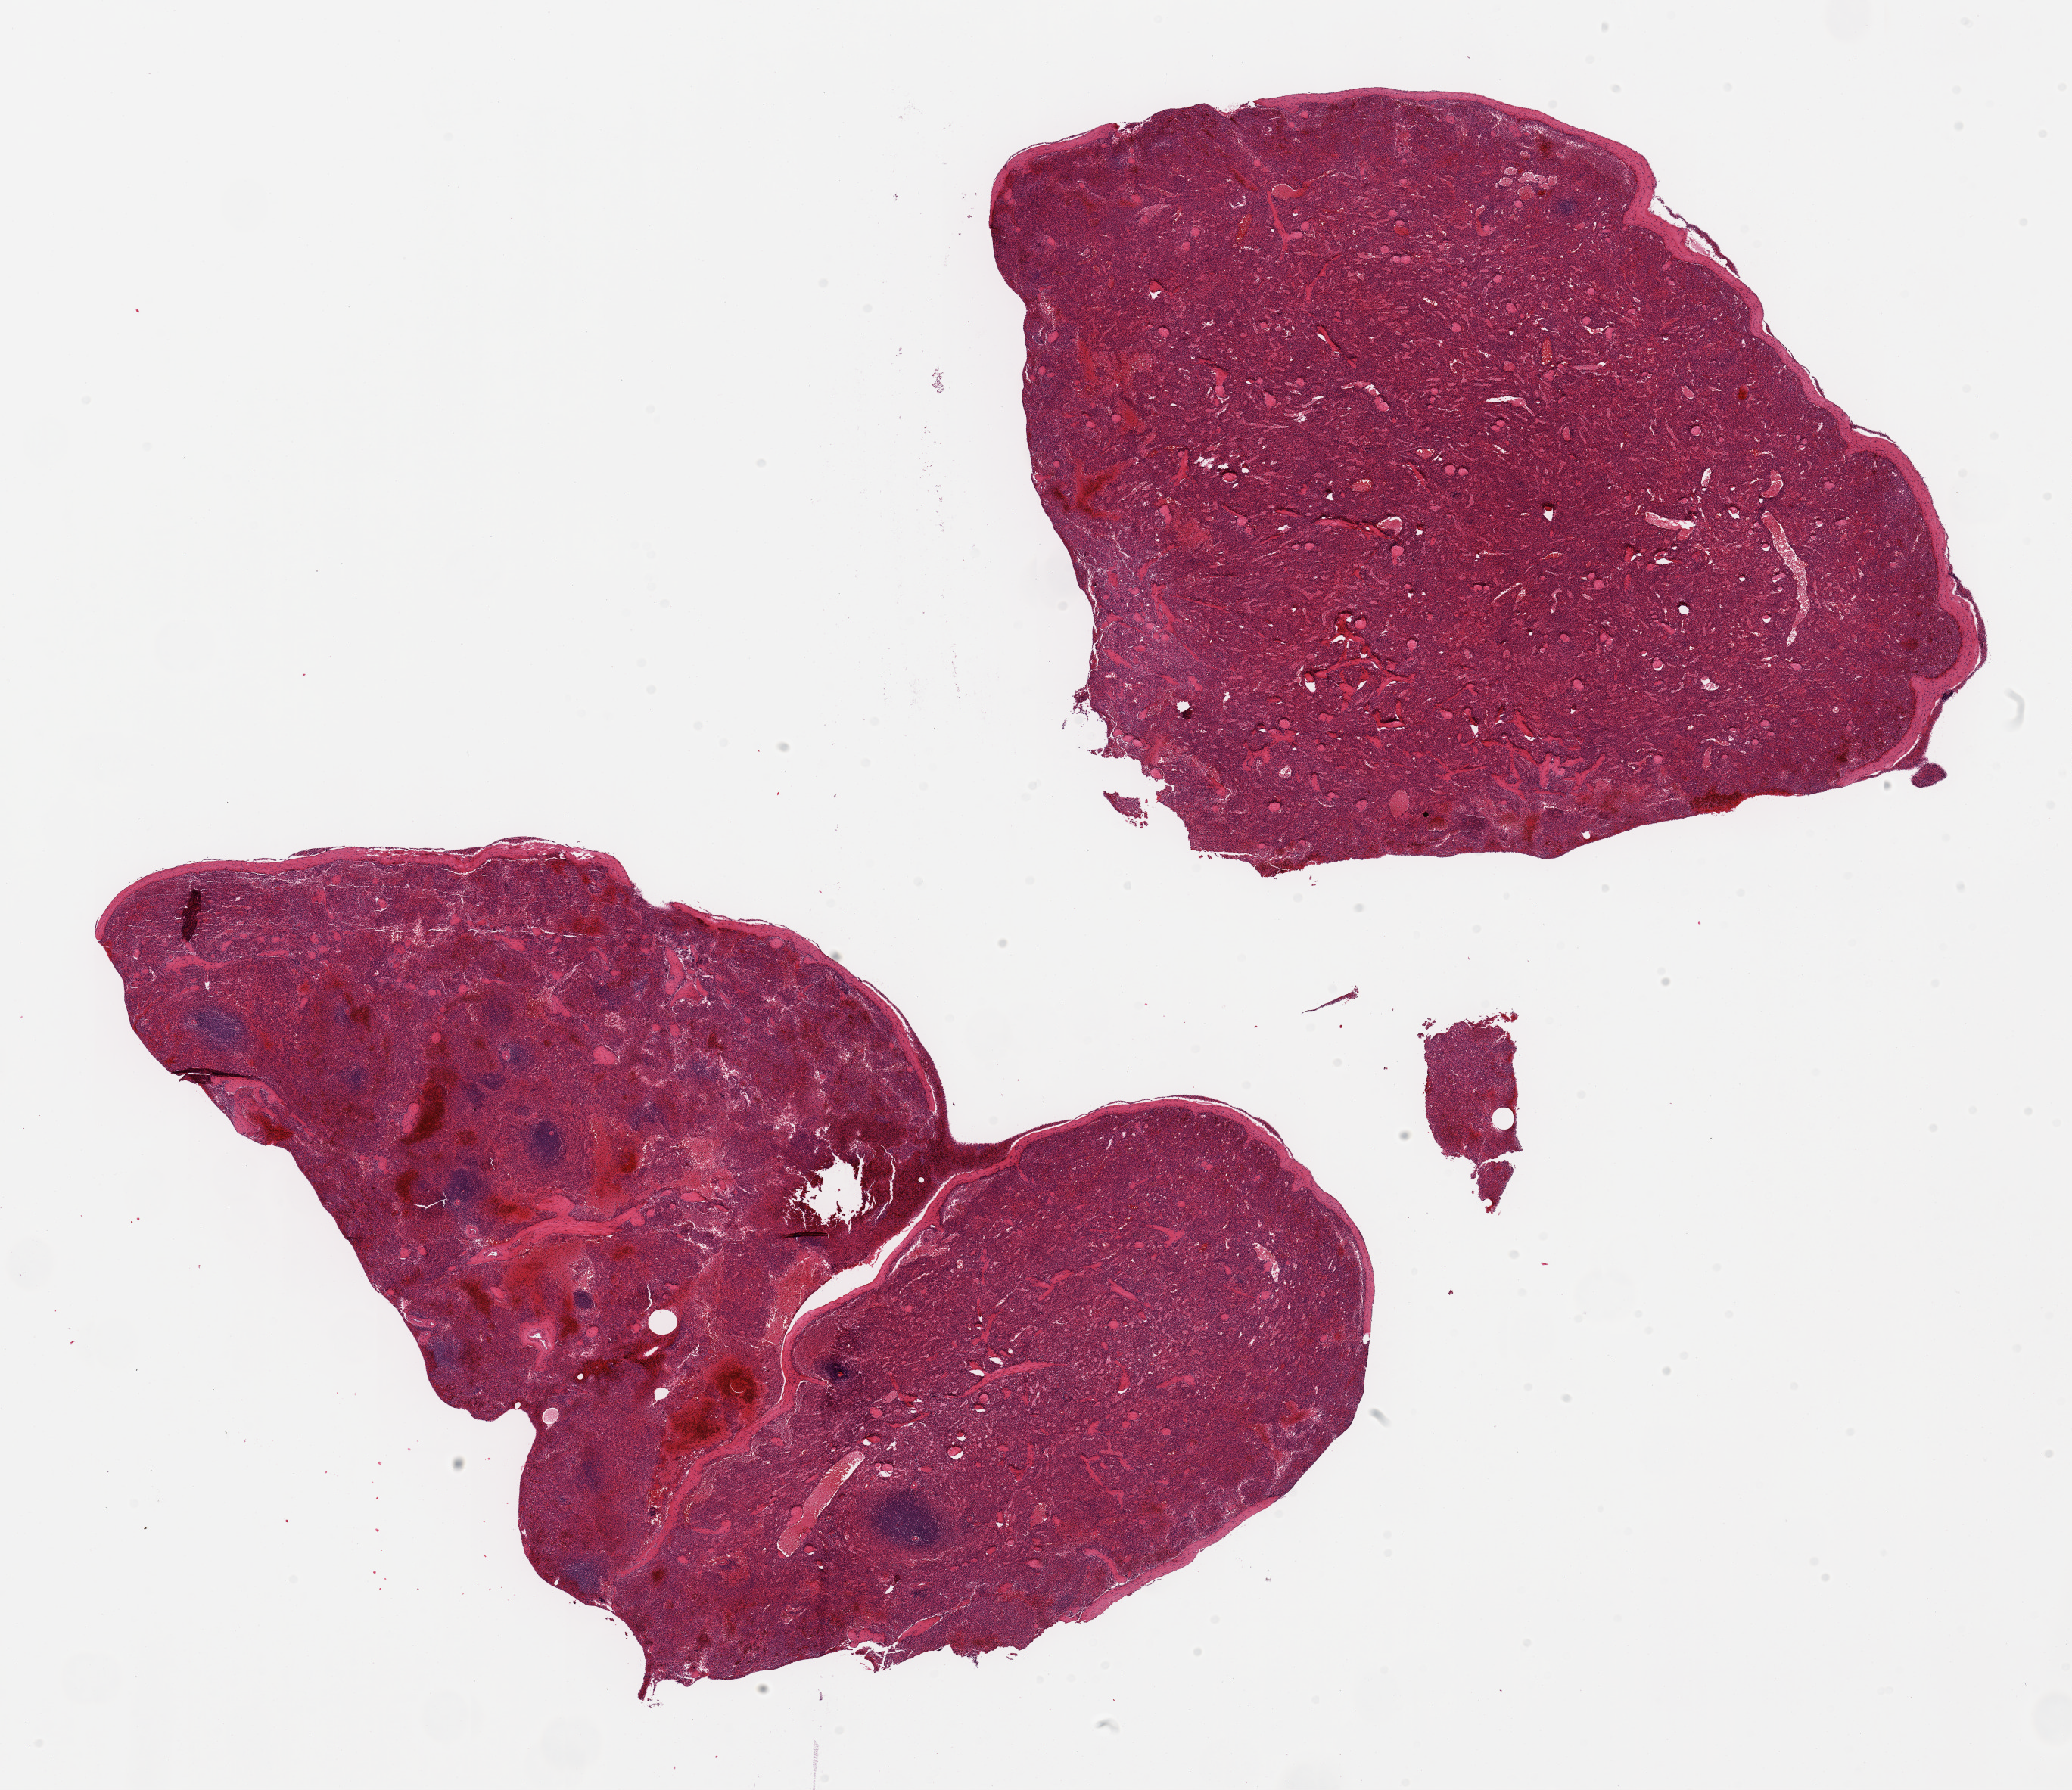
Haematoxylin and eosin whole-slide image — a low-resolution overview of the entire scanned area, about 21.7 x 18.7 mm (acquisition: 20x scan). PAXgene-fixed paraffin-embedded (PFPE) section. Target tissue: spleen. Donor tissue sample.
* review note (as recorded): 2 pieces, no abnormalities